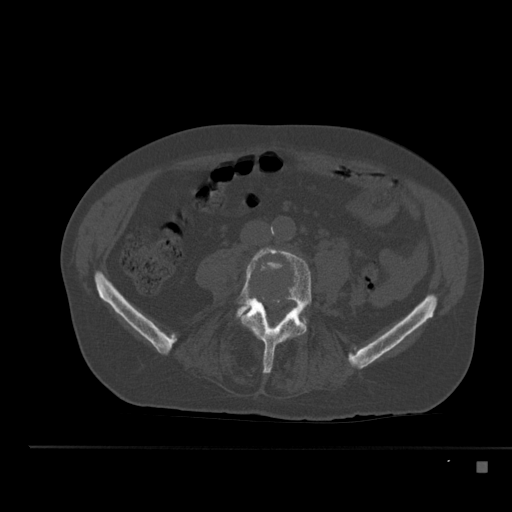
CT including the spine, one axial slice; slice 140 of 517 in the series (ordered by position); 120 kVp; bone window (W 1800 / L 400 HU); 1.5 mm slice thickness; 512 × 512 image matrix. Male patient, age 70 years. From the clinical record (not read from this slice): primary cancer: renal.
Annotated regions visible in this slice (semi-automatic segmentation, software-assisted and operator-edited):
- L4 vertebra: bounding box (x1, y1, x2, y2) in pixels: (237, 247, 312, 374)
- L5 vertebra: (237, 305, 306, 321)